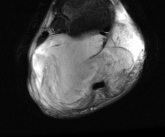
MRI of an extremity soft-tissue mass, one axial slice. Position 19 of 81 along the scan axis. T2-weighted fat-saturated. MR volume resampled by the dataset authors to the PET/CT grid (not the native acquisition matrix). 165 × 137 image matrix, field of view 161 × 134 mm. Male patient. Case-level facts recorded for this patient, not image findings: histological type: liposarcoma - round cell; grade: high; site of the primary tumour: right calf.
Outlined on this slice (expert contour drawn on MRI and transferred to this co-registered scan by the dataset authors):
- gross tumour volume (mass): bounding box [x1, y1, x2, y2] px = [32, 23, 138, 110]